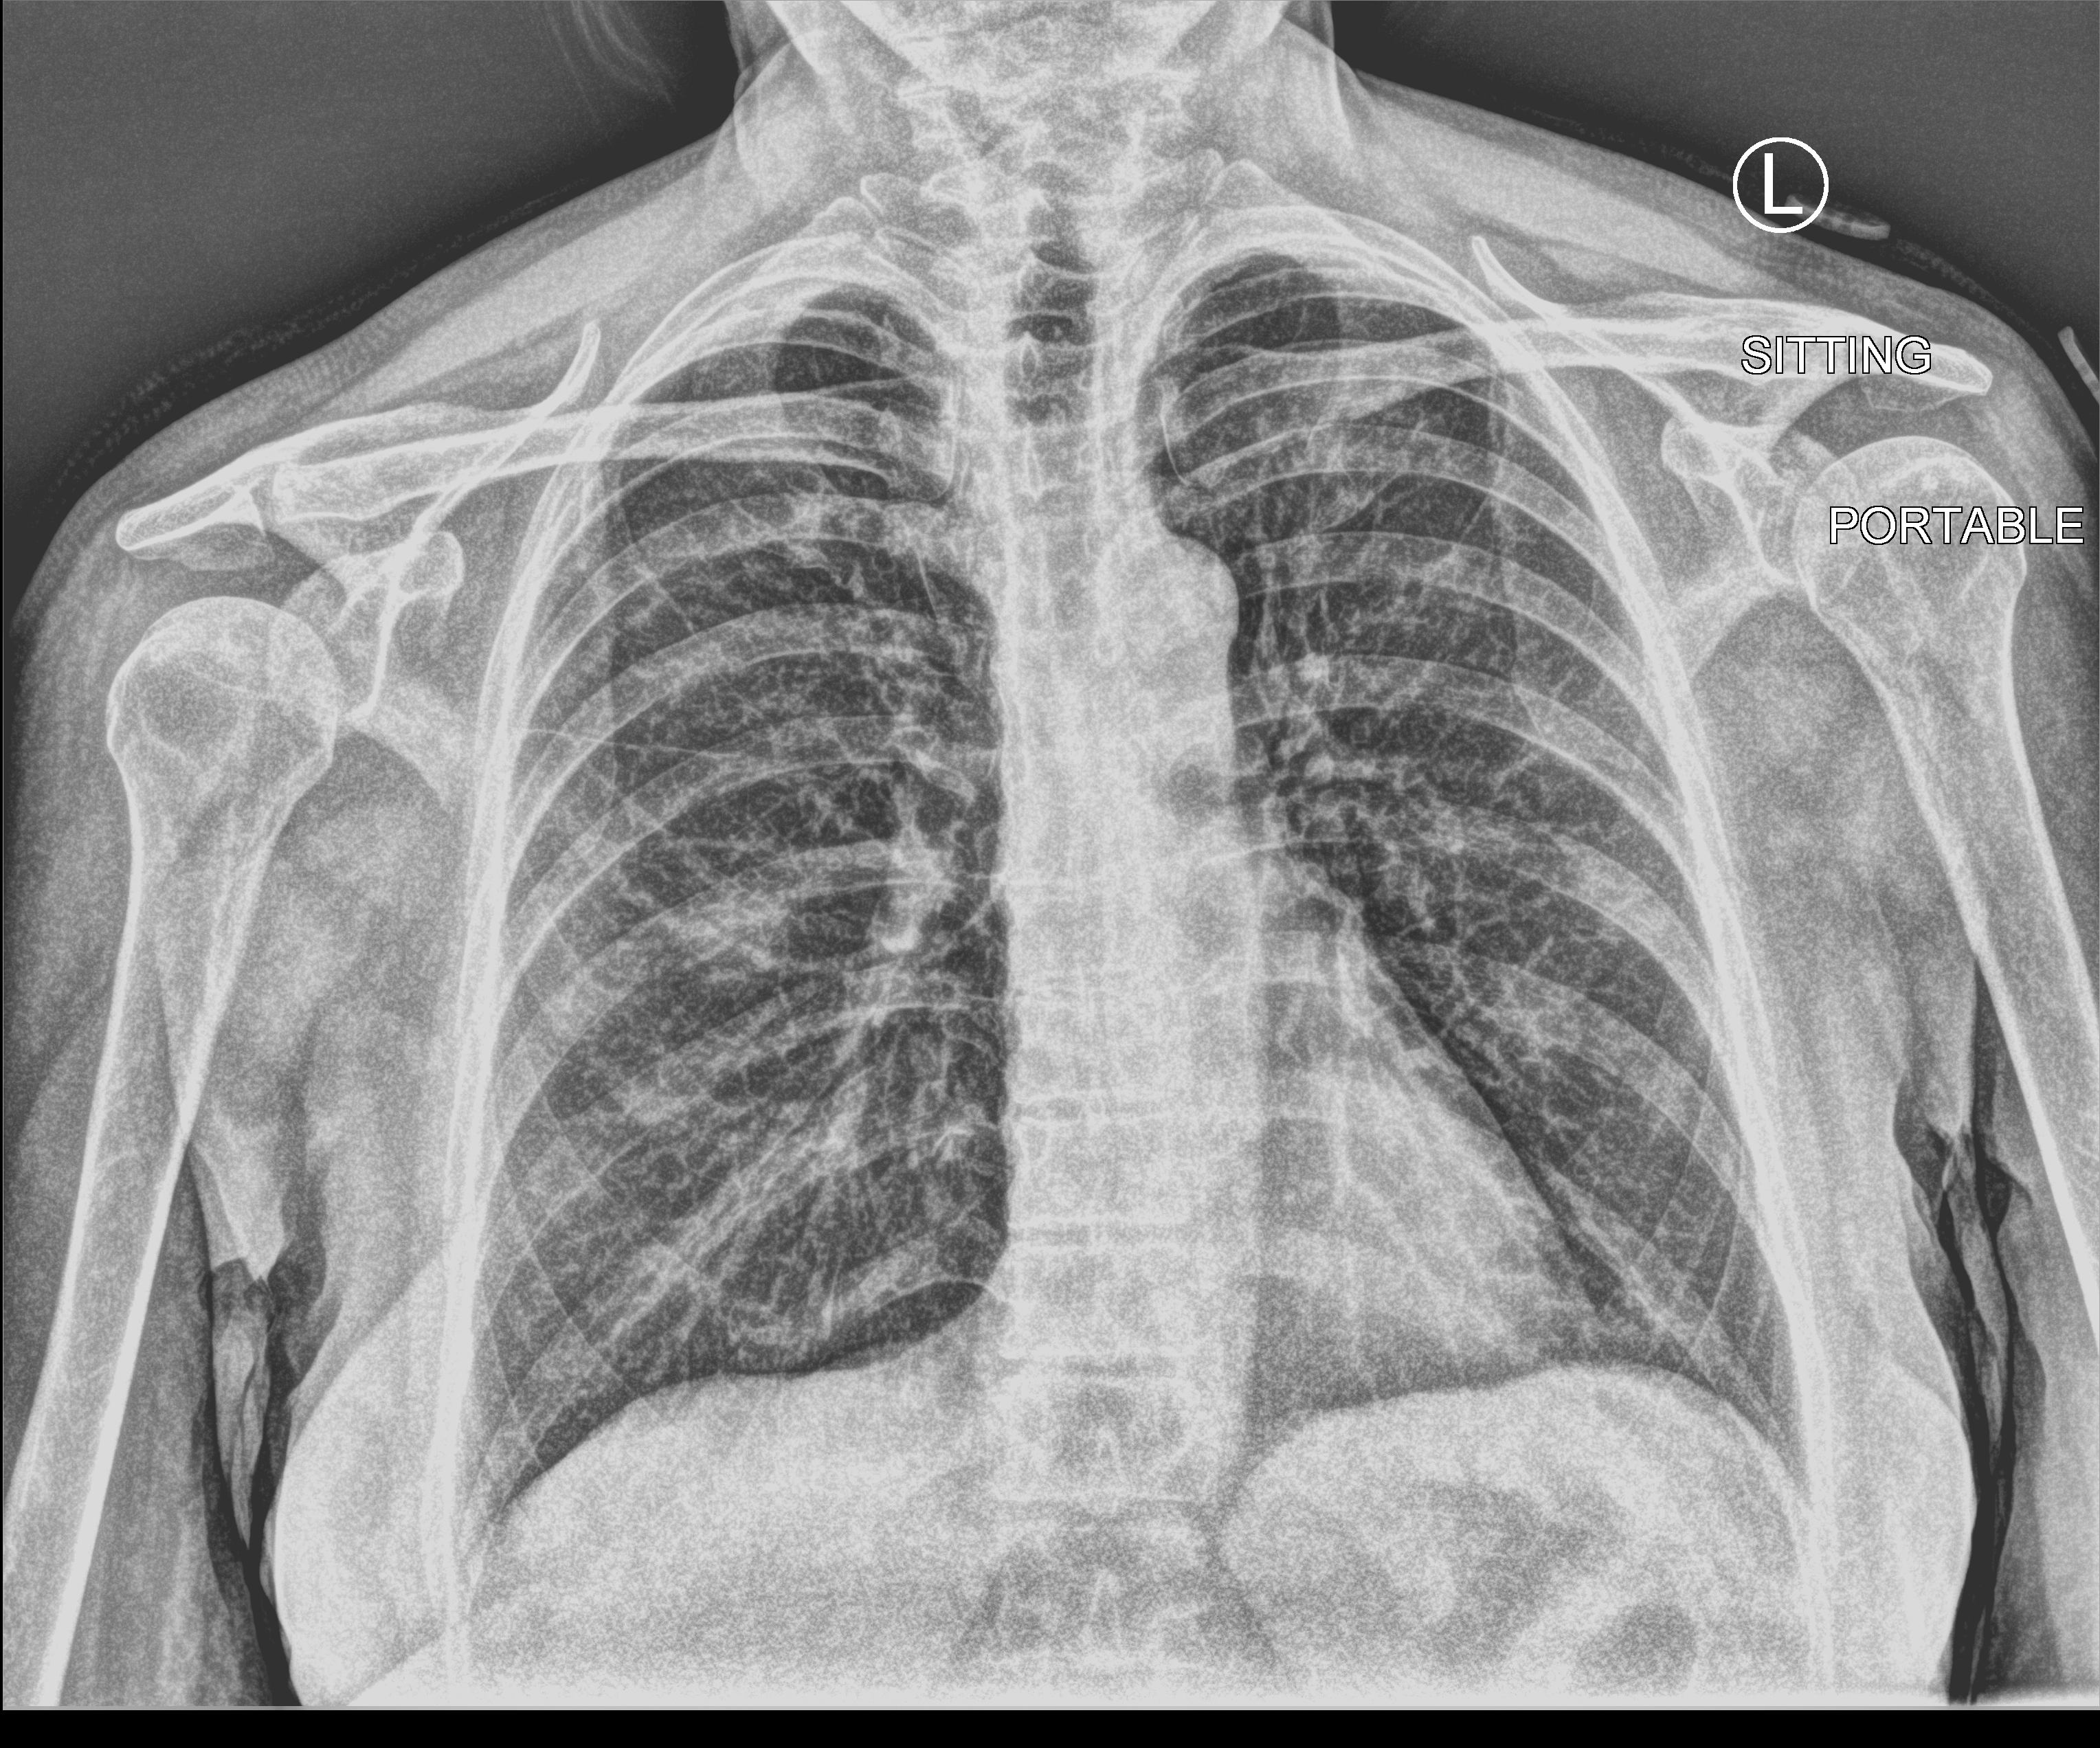
Chest X-ray (portable); anteroposterior (AP) projection. Female patient hospitalised with COVID-19, age 60–74 years.
Admission-level facts for this patient (not findings on this image; timing relative to this image not recorded):
- admitted to intensive care during this hospital stay: no
- mechanically ventilated during this hospital stay: no